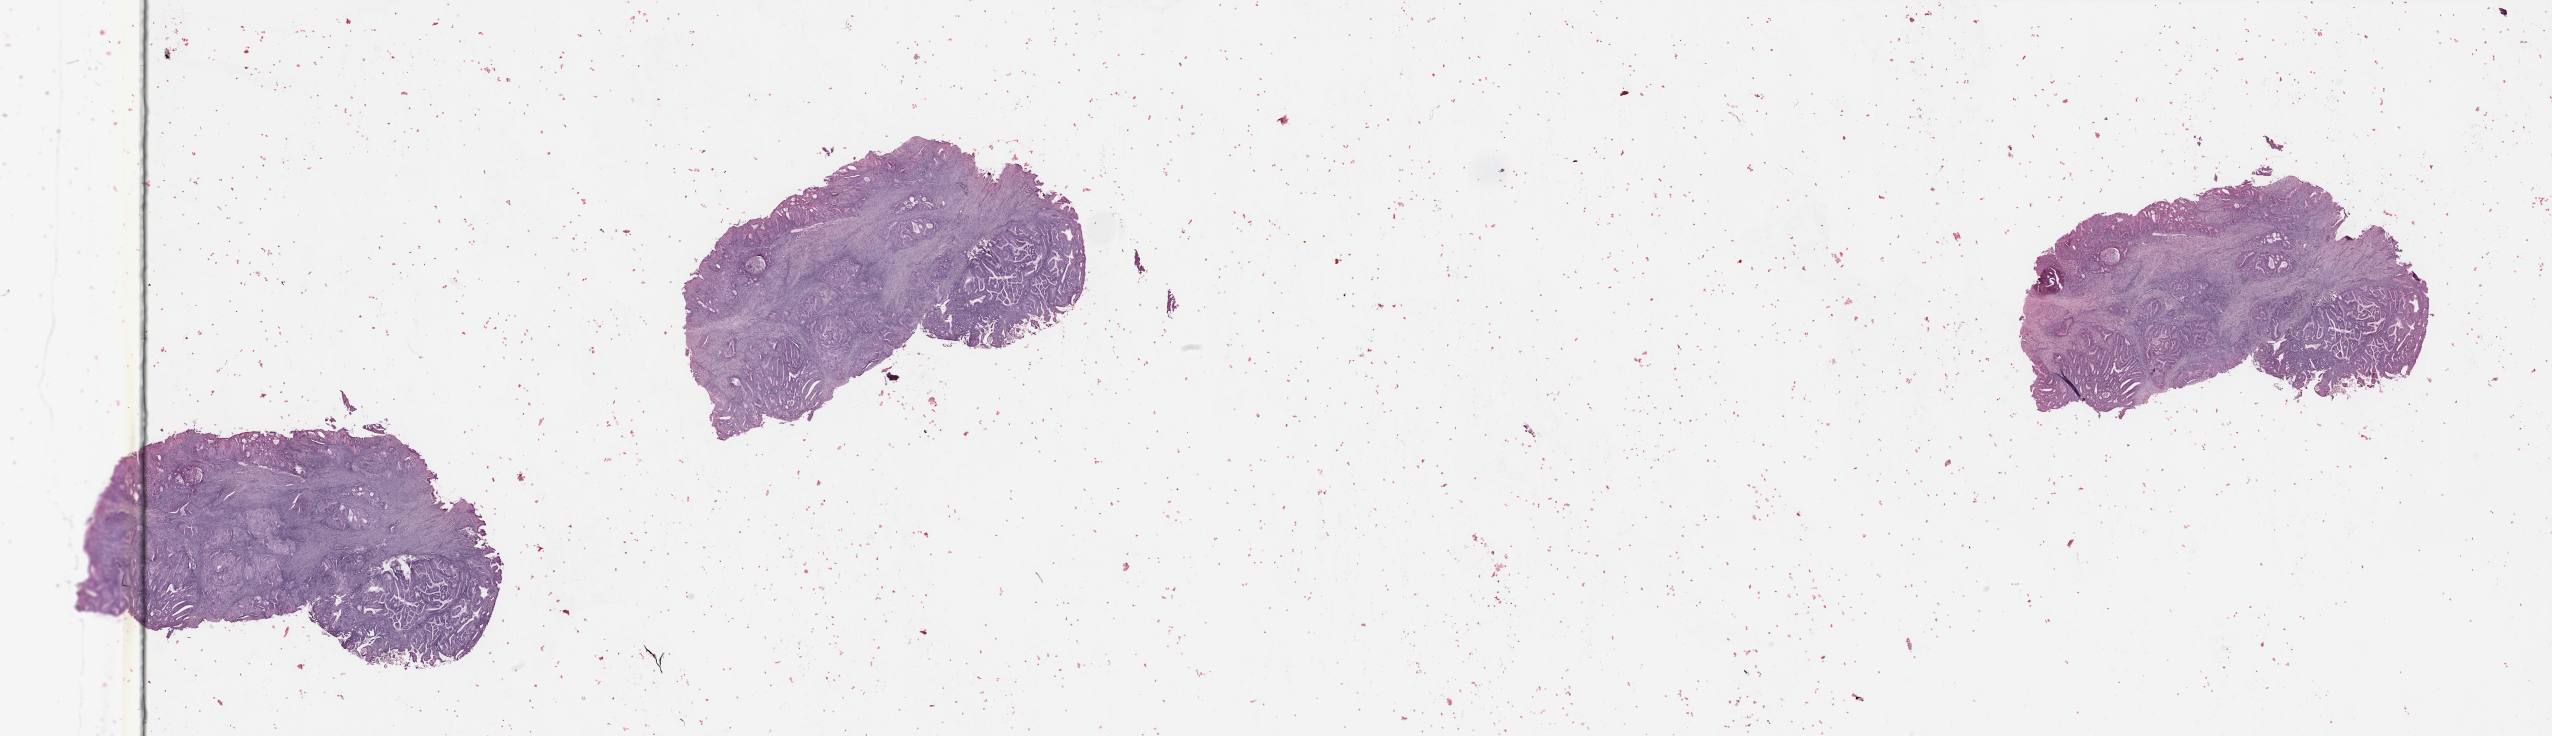
Digitized Hematoxylin and eosin (H&E) stained tissue section (whole slide) — a low-resolution overview of the entire scanned area, about 40.4 x 11.6 mm, tumour tissue sample, uterus. 41-year-old female patient. Histologic grade: G3 (poorly differentiated).
AJCC pathologic stage: IV. Histologic diagnosis: Endometrioid adenocarcinoma, NOS.